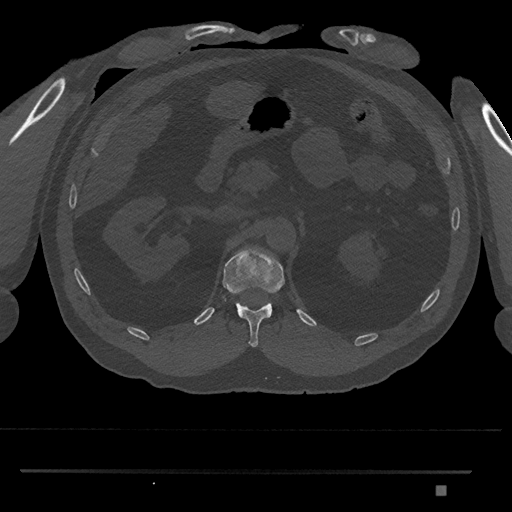
CT including the spine, one axial slice; slice 873 of 1134 in the series (ordered by position); bone window (W 1800 / L 400 HU); 0.5 mm slice thickness; 512 × 512 image matrix, field of view 429 × 429 mm. Patient: male, 65 years. Case-level facts recorded for this patient, not image findings: primary cancer: prostate.
Annotated regions visible in this slice (semi-automatic segmentation, software-assisted and operator-edited):
- T12 vertebra: bounding box (x1, y1, x2, y2) in pixels: (222, 250, 285, 347)